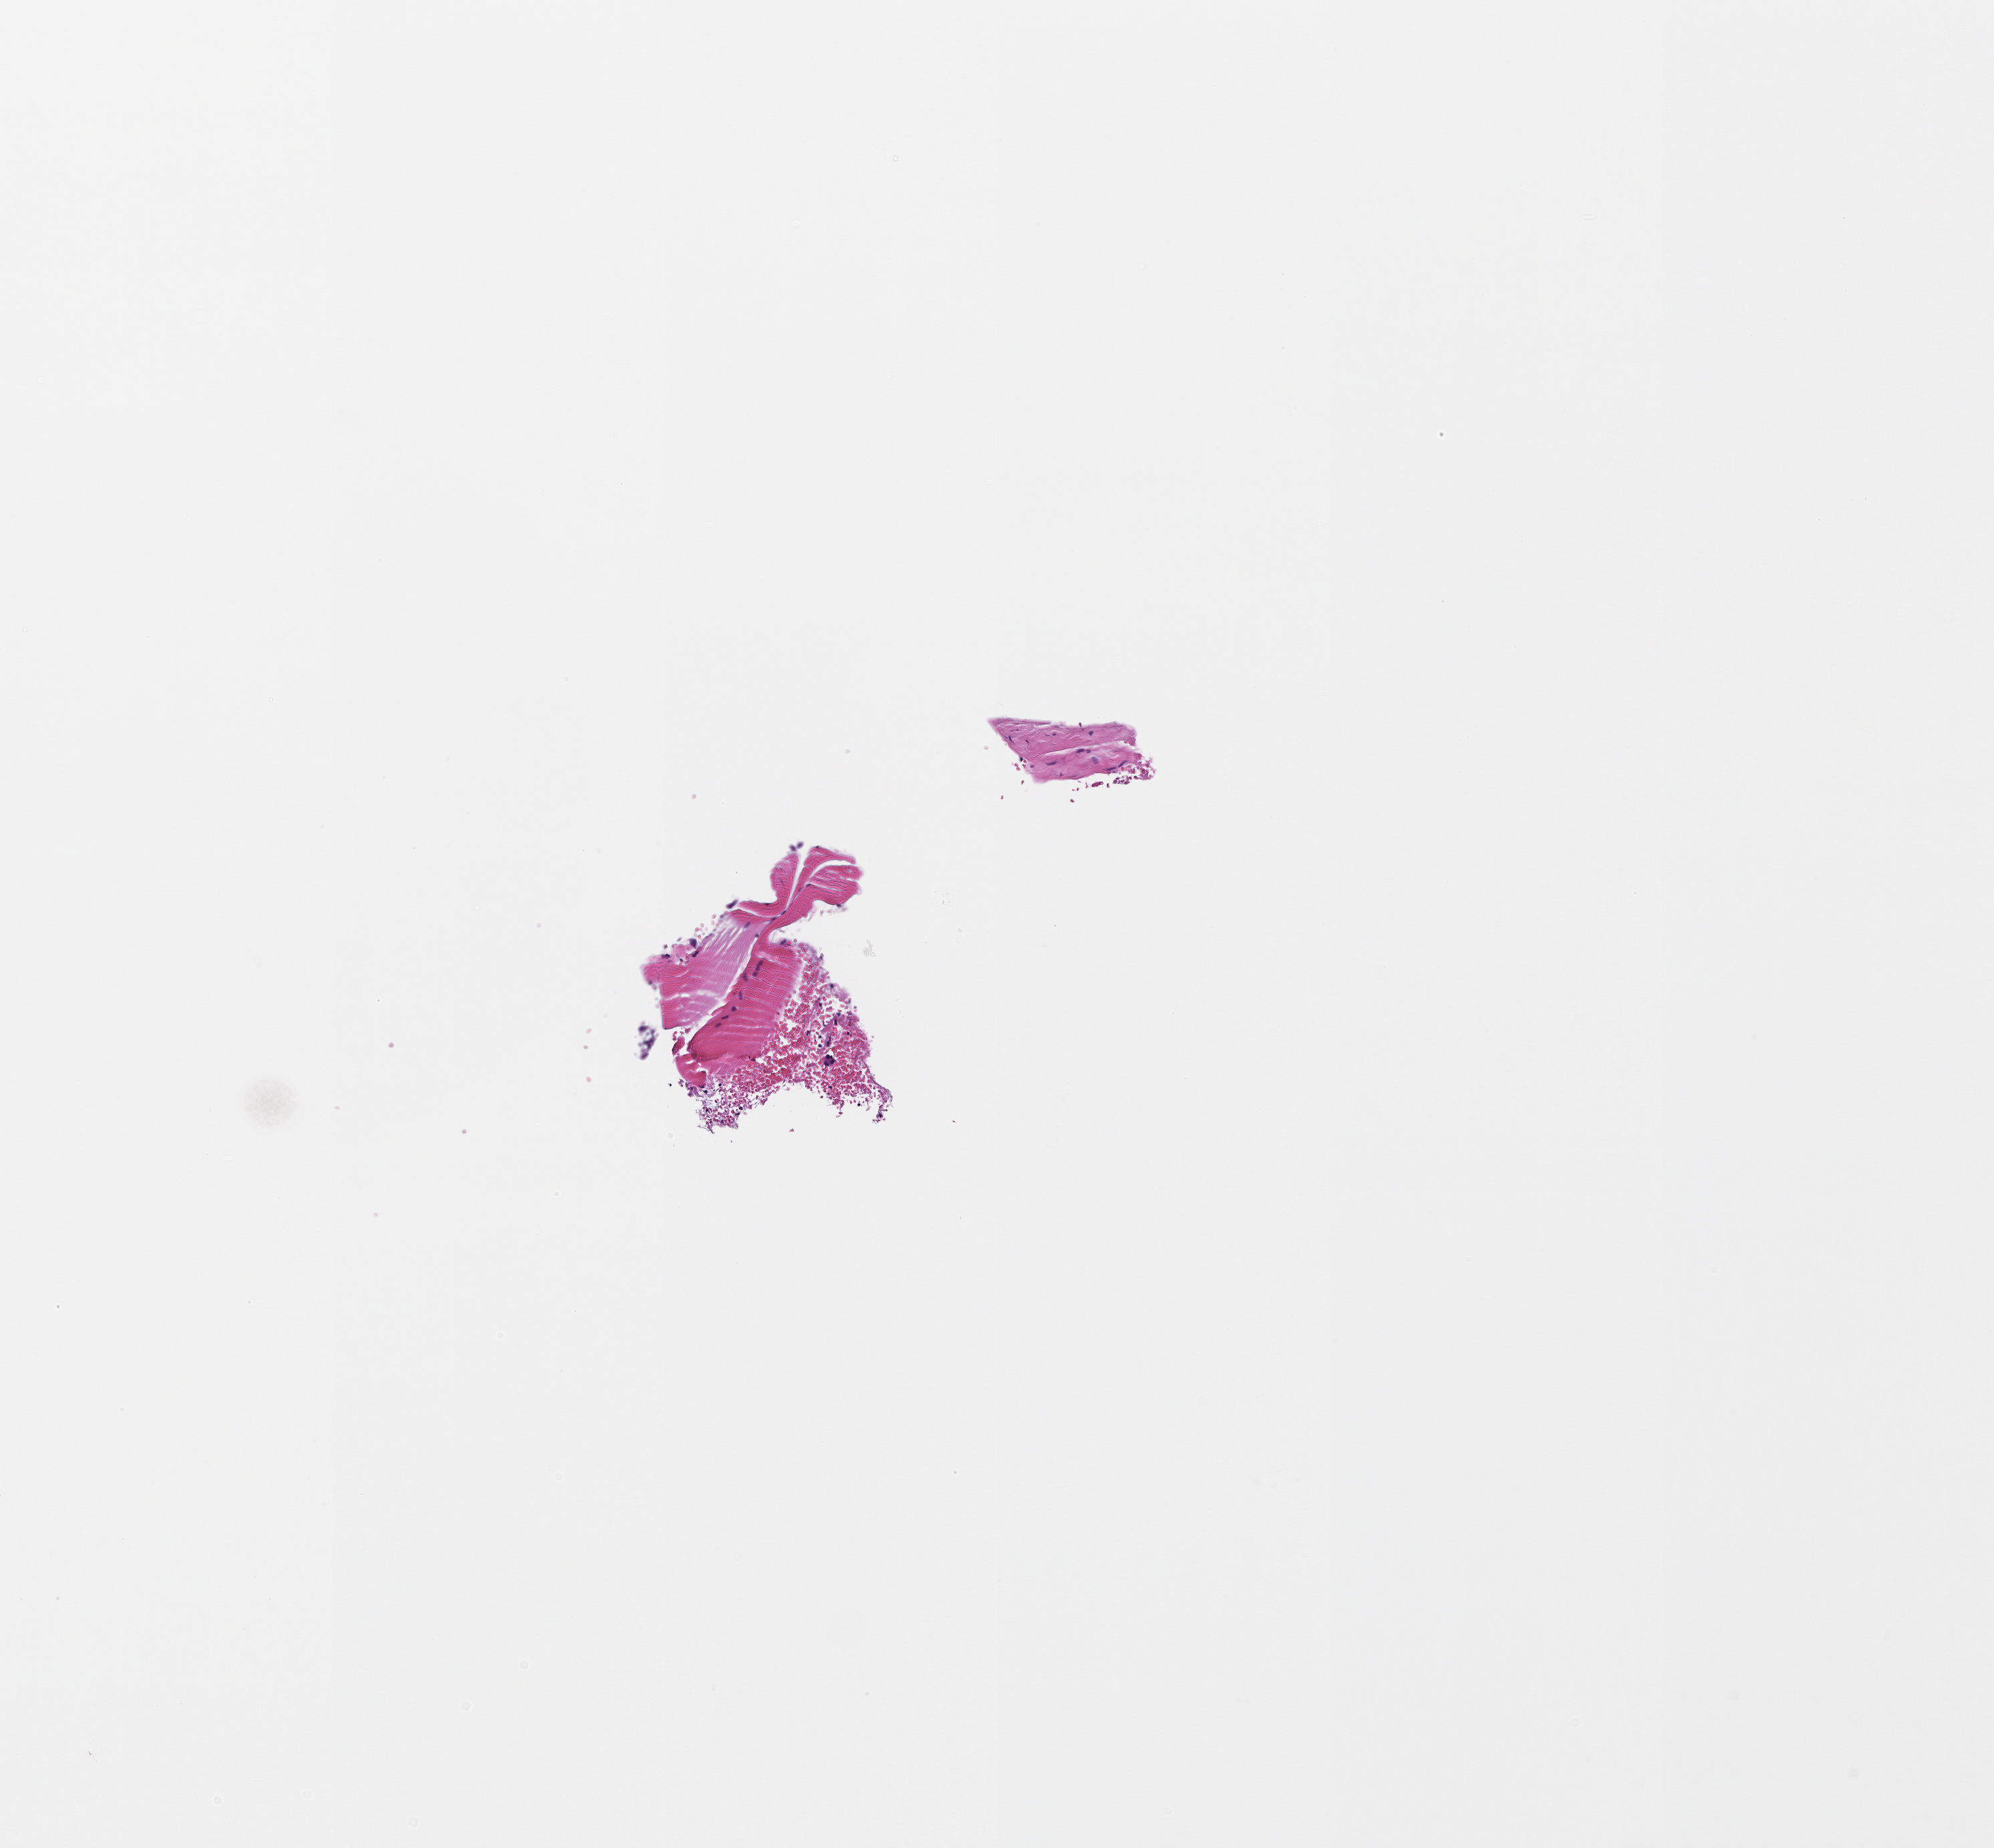
Digitized haematoxylin and eosin-stained section — low-resolution overview of the scanned area, about 3.0 x 2.8 mm. Formalin-fixed paraffin-embedded section. Collected at baseline (before treatment). Male patient.
This section: metastatic tumor tissue. Primary diagnosis of the patient: Melanoma.